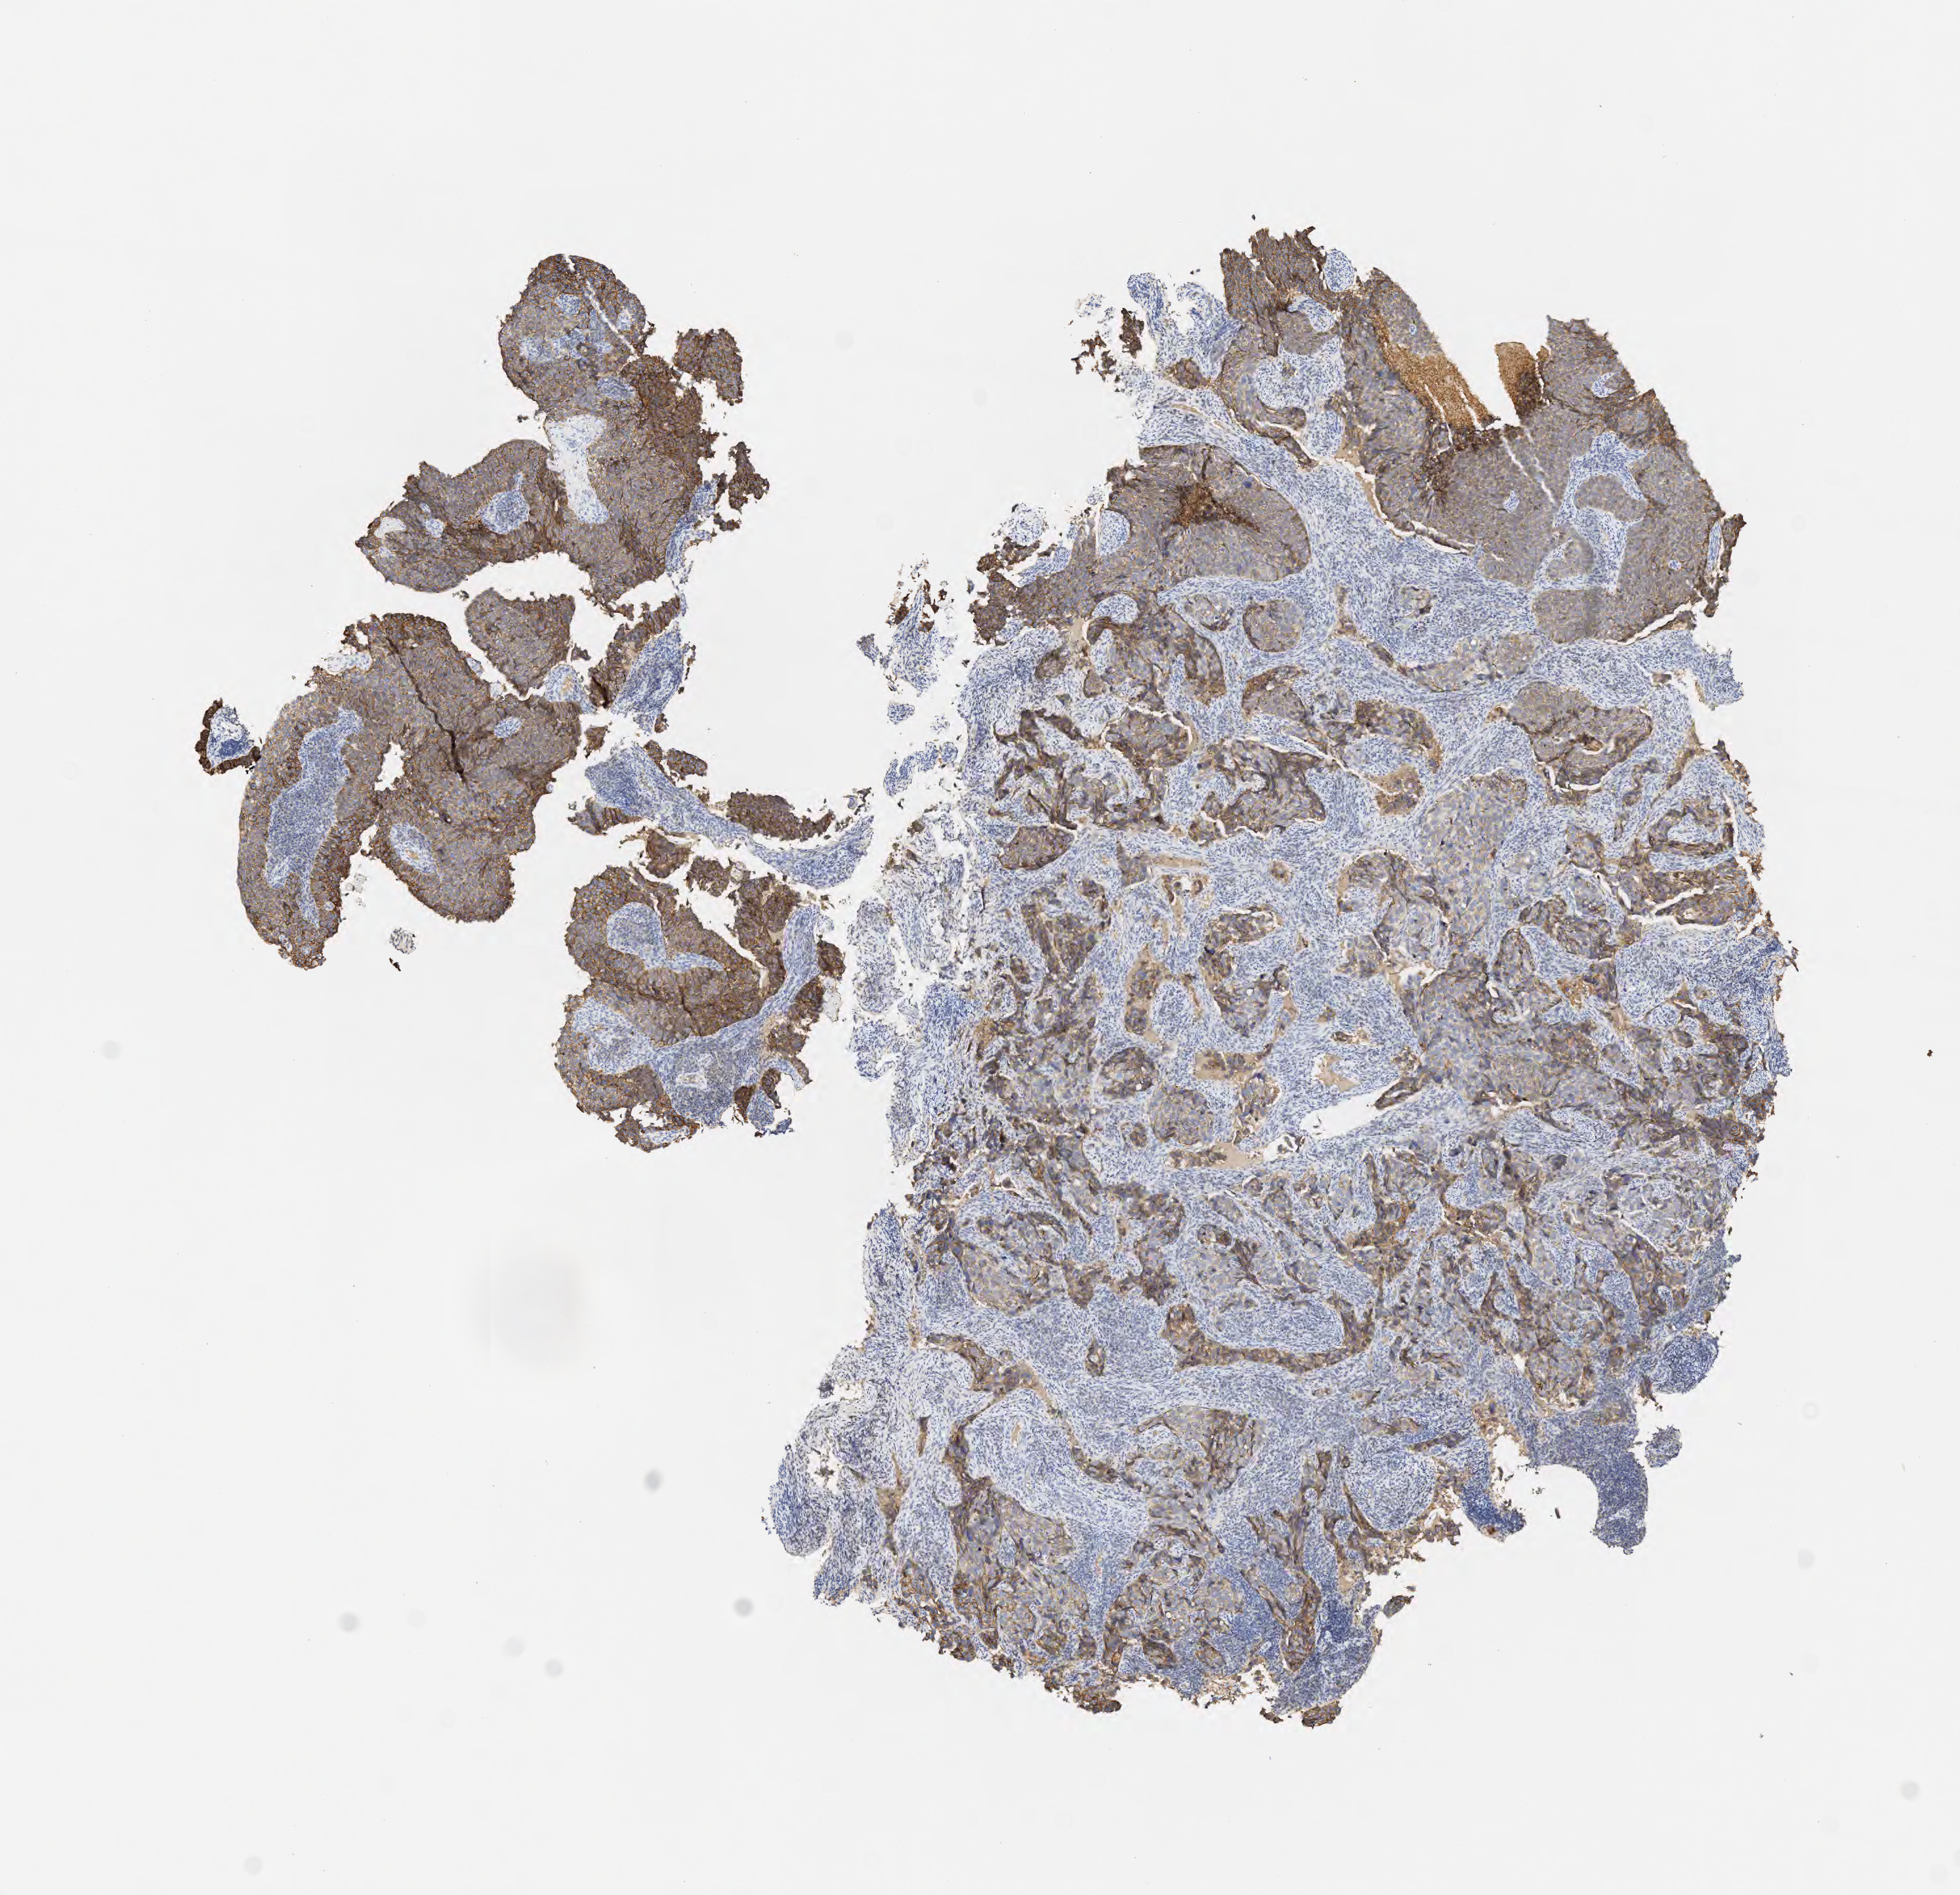
Immunohistochemistry (IHC) whole-slide image stained for Ber-EP4, low-resolution overview of the scanned area, about 6.0 x 5.8 mm. Tumor tissue. Site: cervix. Patient female; age 47 years.
Diagnosis: Squamous cell carcinoma, large cell, nonkeratinizing, NOS.